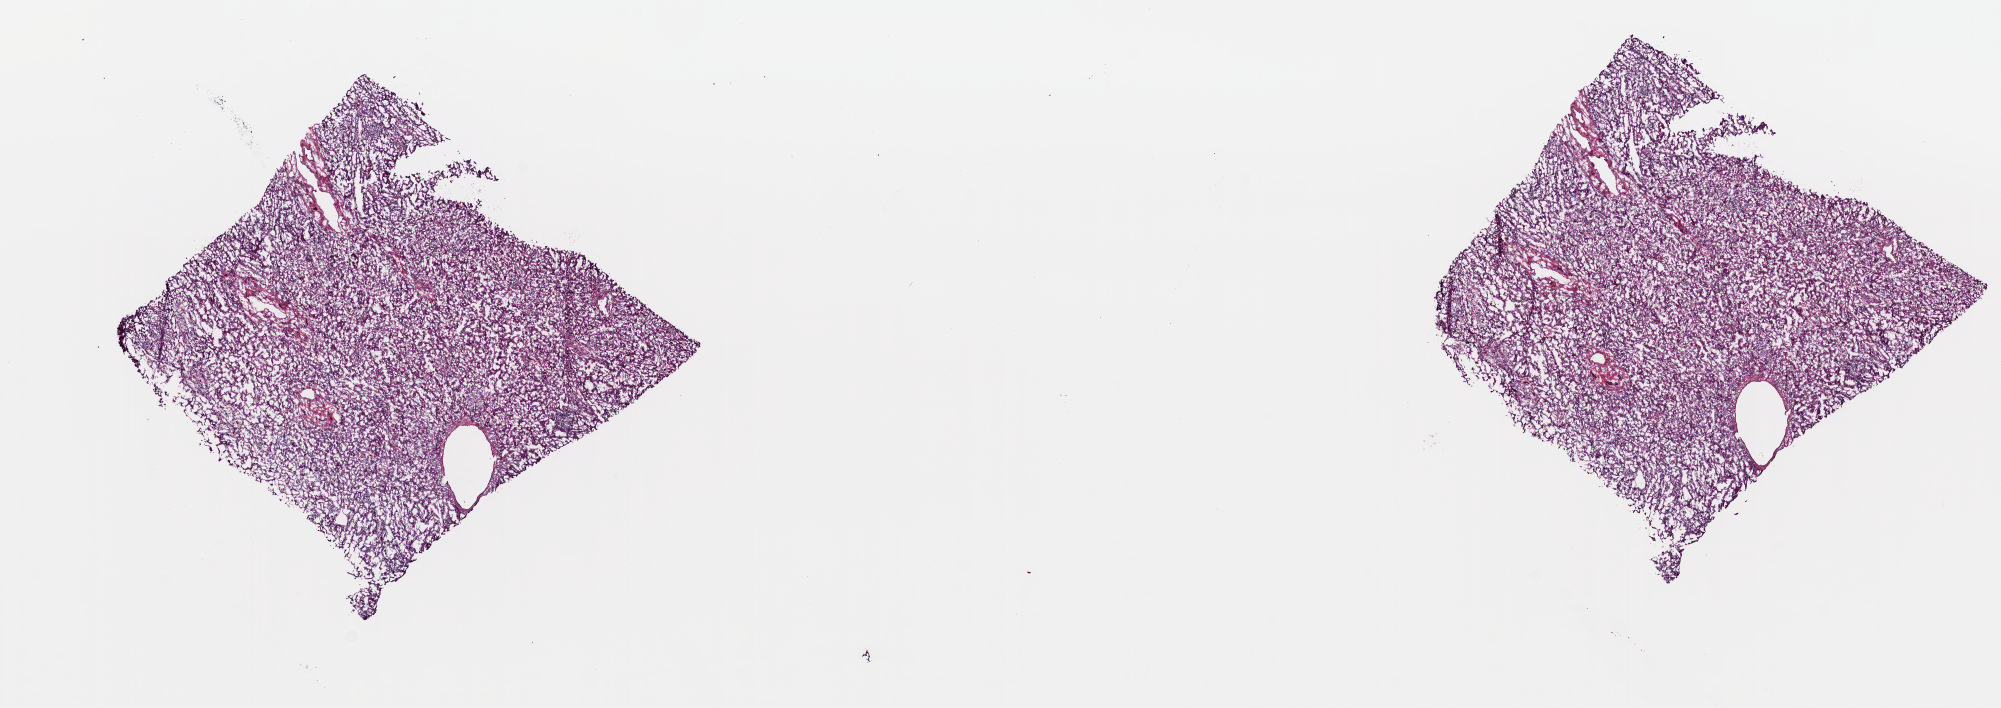
Whole-slide histology image, H&E-stained — shown as a low-resolution overview of the whole scanned area (about 15.9 x 5.6 mm, from a 20x scan); frozen section from the top of the tissue portion; solid tissue normal (non-tumour tissue) sample from the liver. Male patient; age at initial diagnosis 69 years. Slide review estimates, as recorded: tumour cells 0%, tumour nuclei 0%, normal cells 90%, stromal cells 10%, necrosis 0%. Infiltration values recorded for this section: lymphocyte infiltration 25%, monocyte infiltration 0%, neutrophil infiltration 0%.
This section: solid tissue normal (non-tumour) sample from the same patient. Patient diagnosis: Hepatocellular carcinoma, NOS.